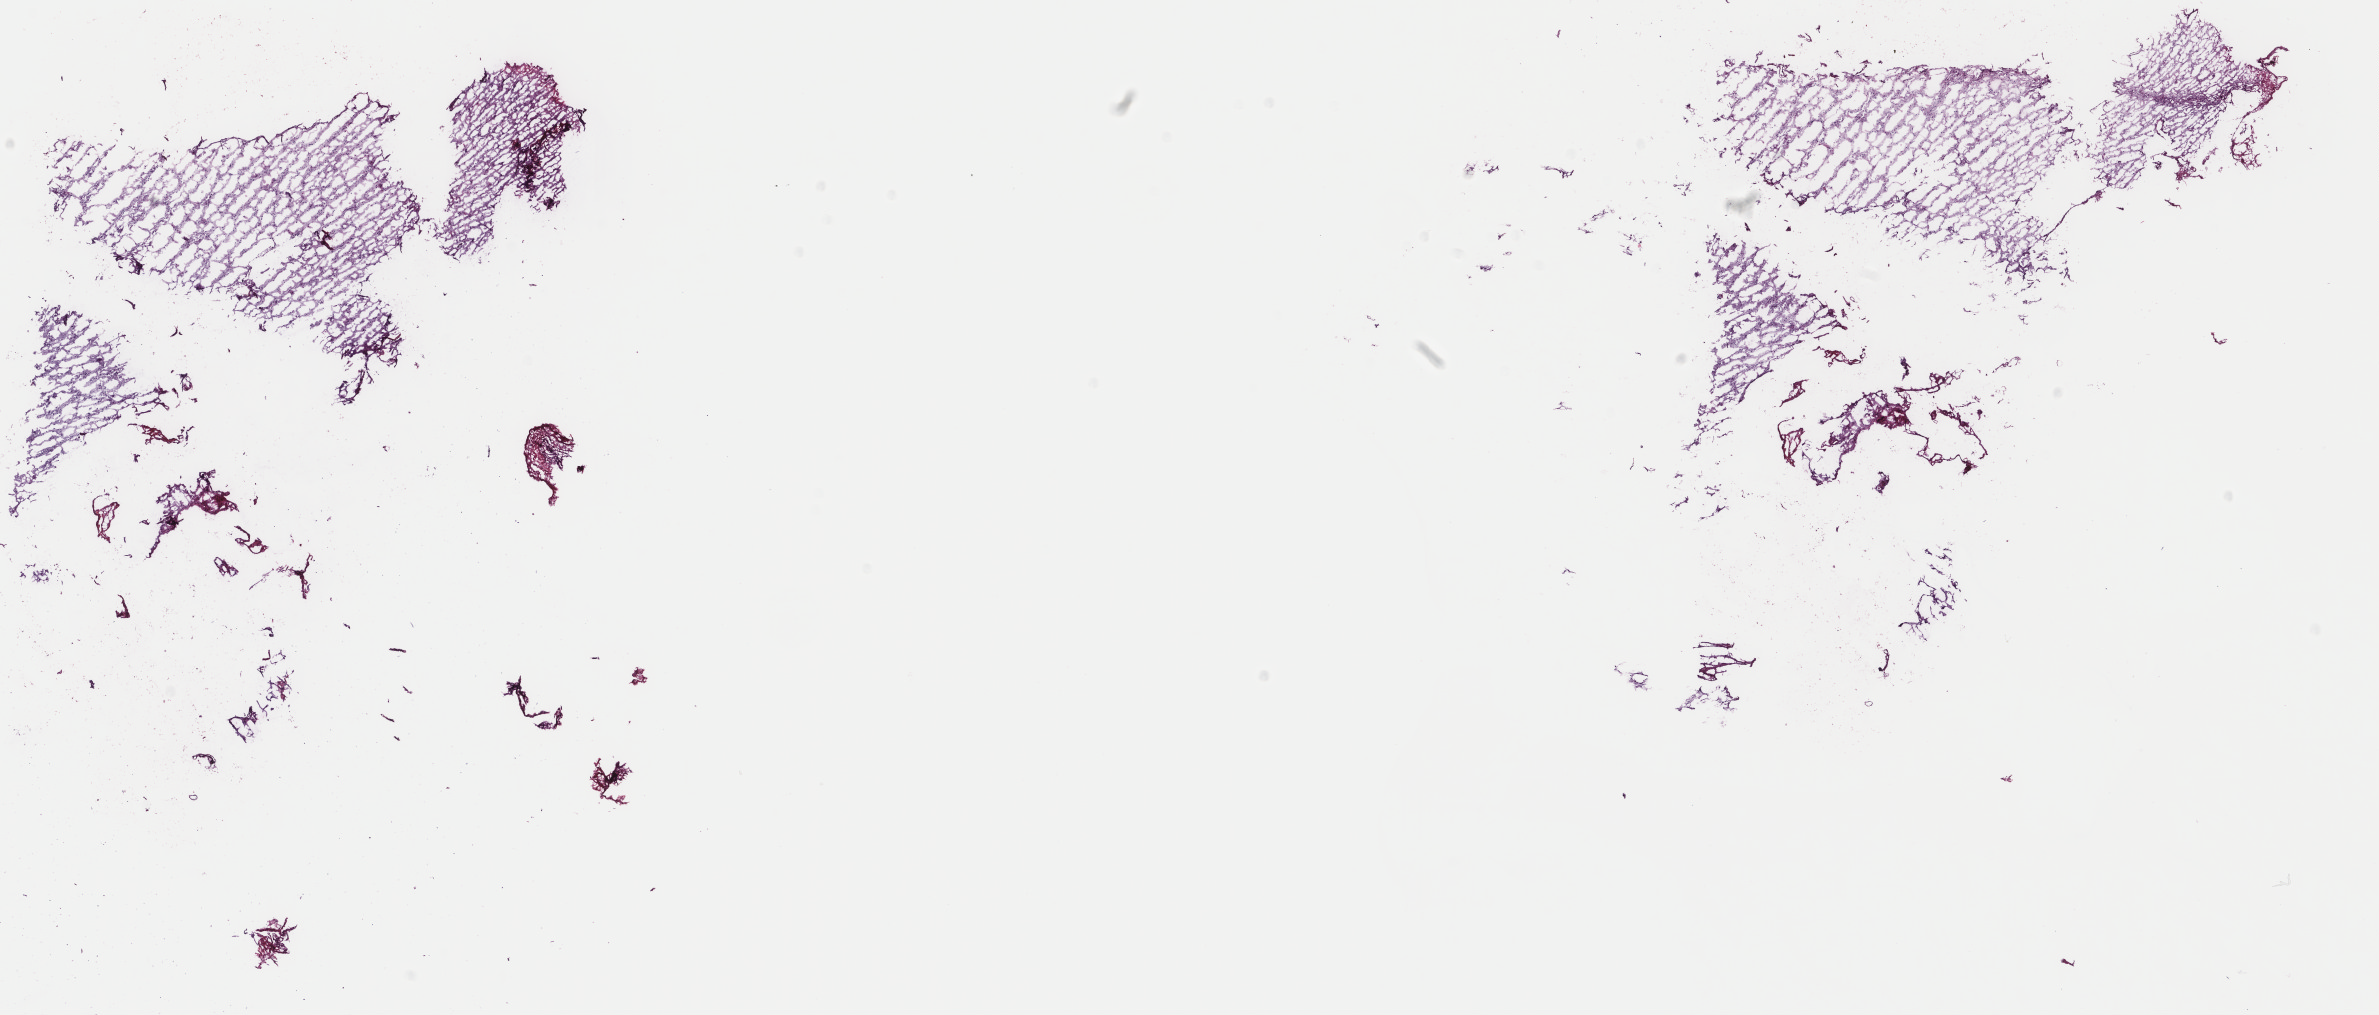
H&E-stained whole-slide image, shown as a low-resolution overview of the whole scanned area (about 18.9 x 8.1 mm, from a 40x scan); frozen section from the top of the tissue portion; primary tumour sample from the brain. Patient: female, age at initial diagnosis 59 years. Histologic grade: G2 (moderately differentiated). Pathologist review of this section (percent, as recorded): tumour cells 20%, tumour nuclei 70%, normal cells 10%, stromal cells 70%, necrosis 0%. Inflammatory infiltration, as recorded: lymphocyte infiltration 0%, monocyte infiltration 0%, neutrophil infiltration 0%.
- pathologic diagnosis: Mixed glioma